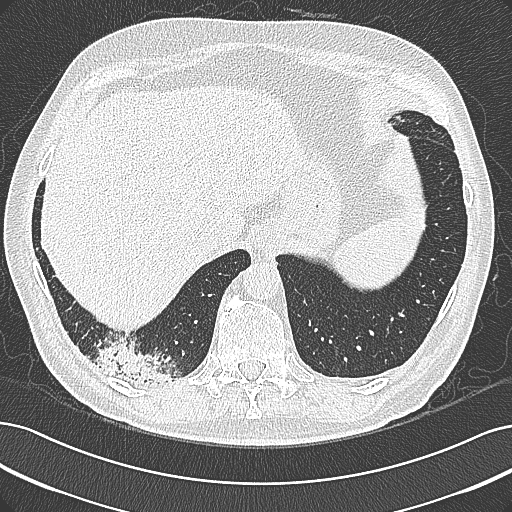
Chest CT (low-dose screening protocol), one axial image; baseline screening round; lung window (W 1500 / L -600 HU); 1 mm slice thickness; lung (sharp) reconstruction kernel (B80f); 120 kVp; 512 × 512 image matrix. Male participant, aged 68 years at enrolment.
Expert reader's lesion annotation, box from (x=95, y=338) to (x=192, y=399) px. Screening reader's record for this exam: no non-calcified nodule ≥4 mm recorded. Official screen result: negative screen, significant abnormalities not suspicious for lung cancer. Participant outcome: lung cancer diagnosed 154 days after this screen — mucinous adenocarcinoma, right lower lobe, well differentiated (G1), stage IB (AJCC 6th edition), 50 mm at pathology.